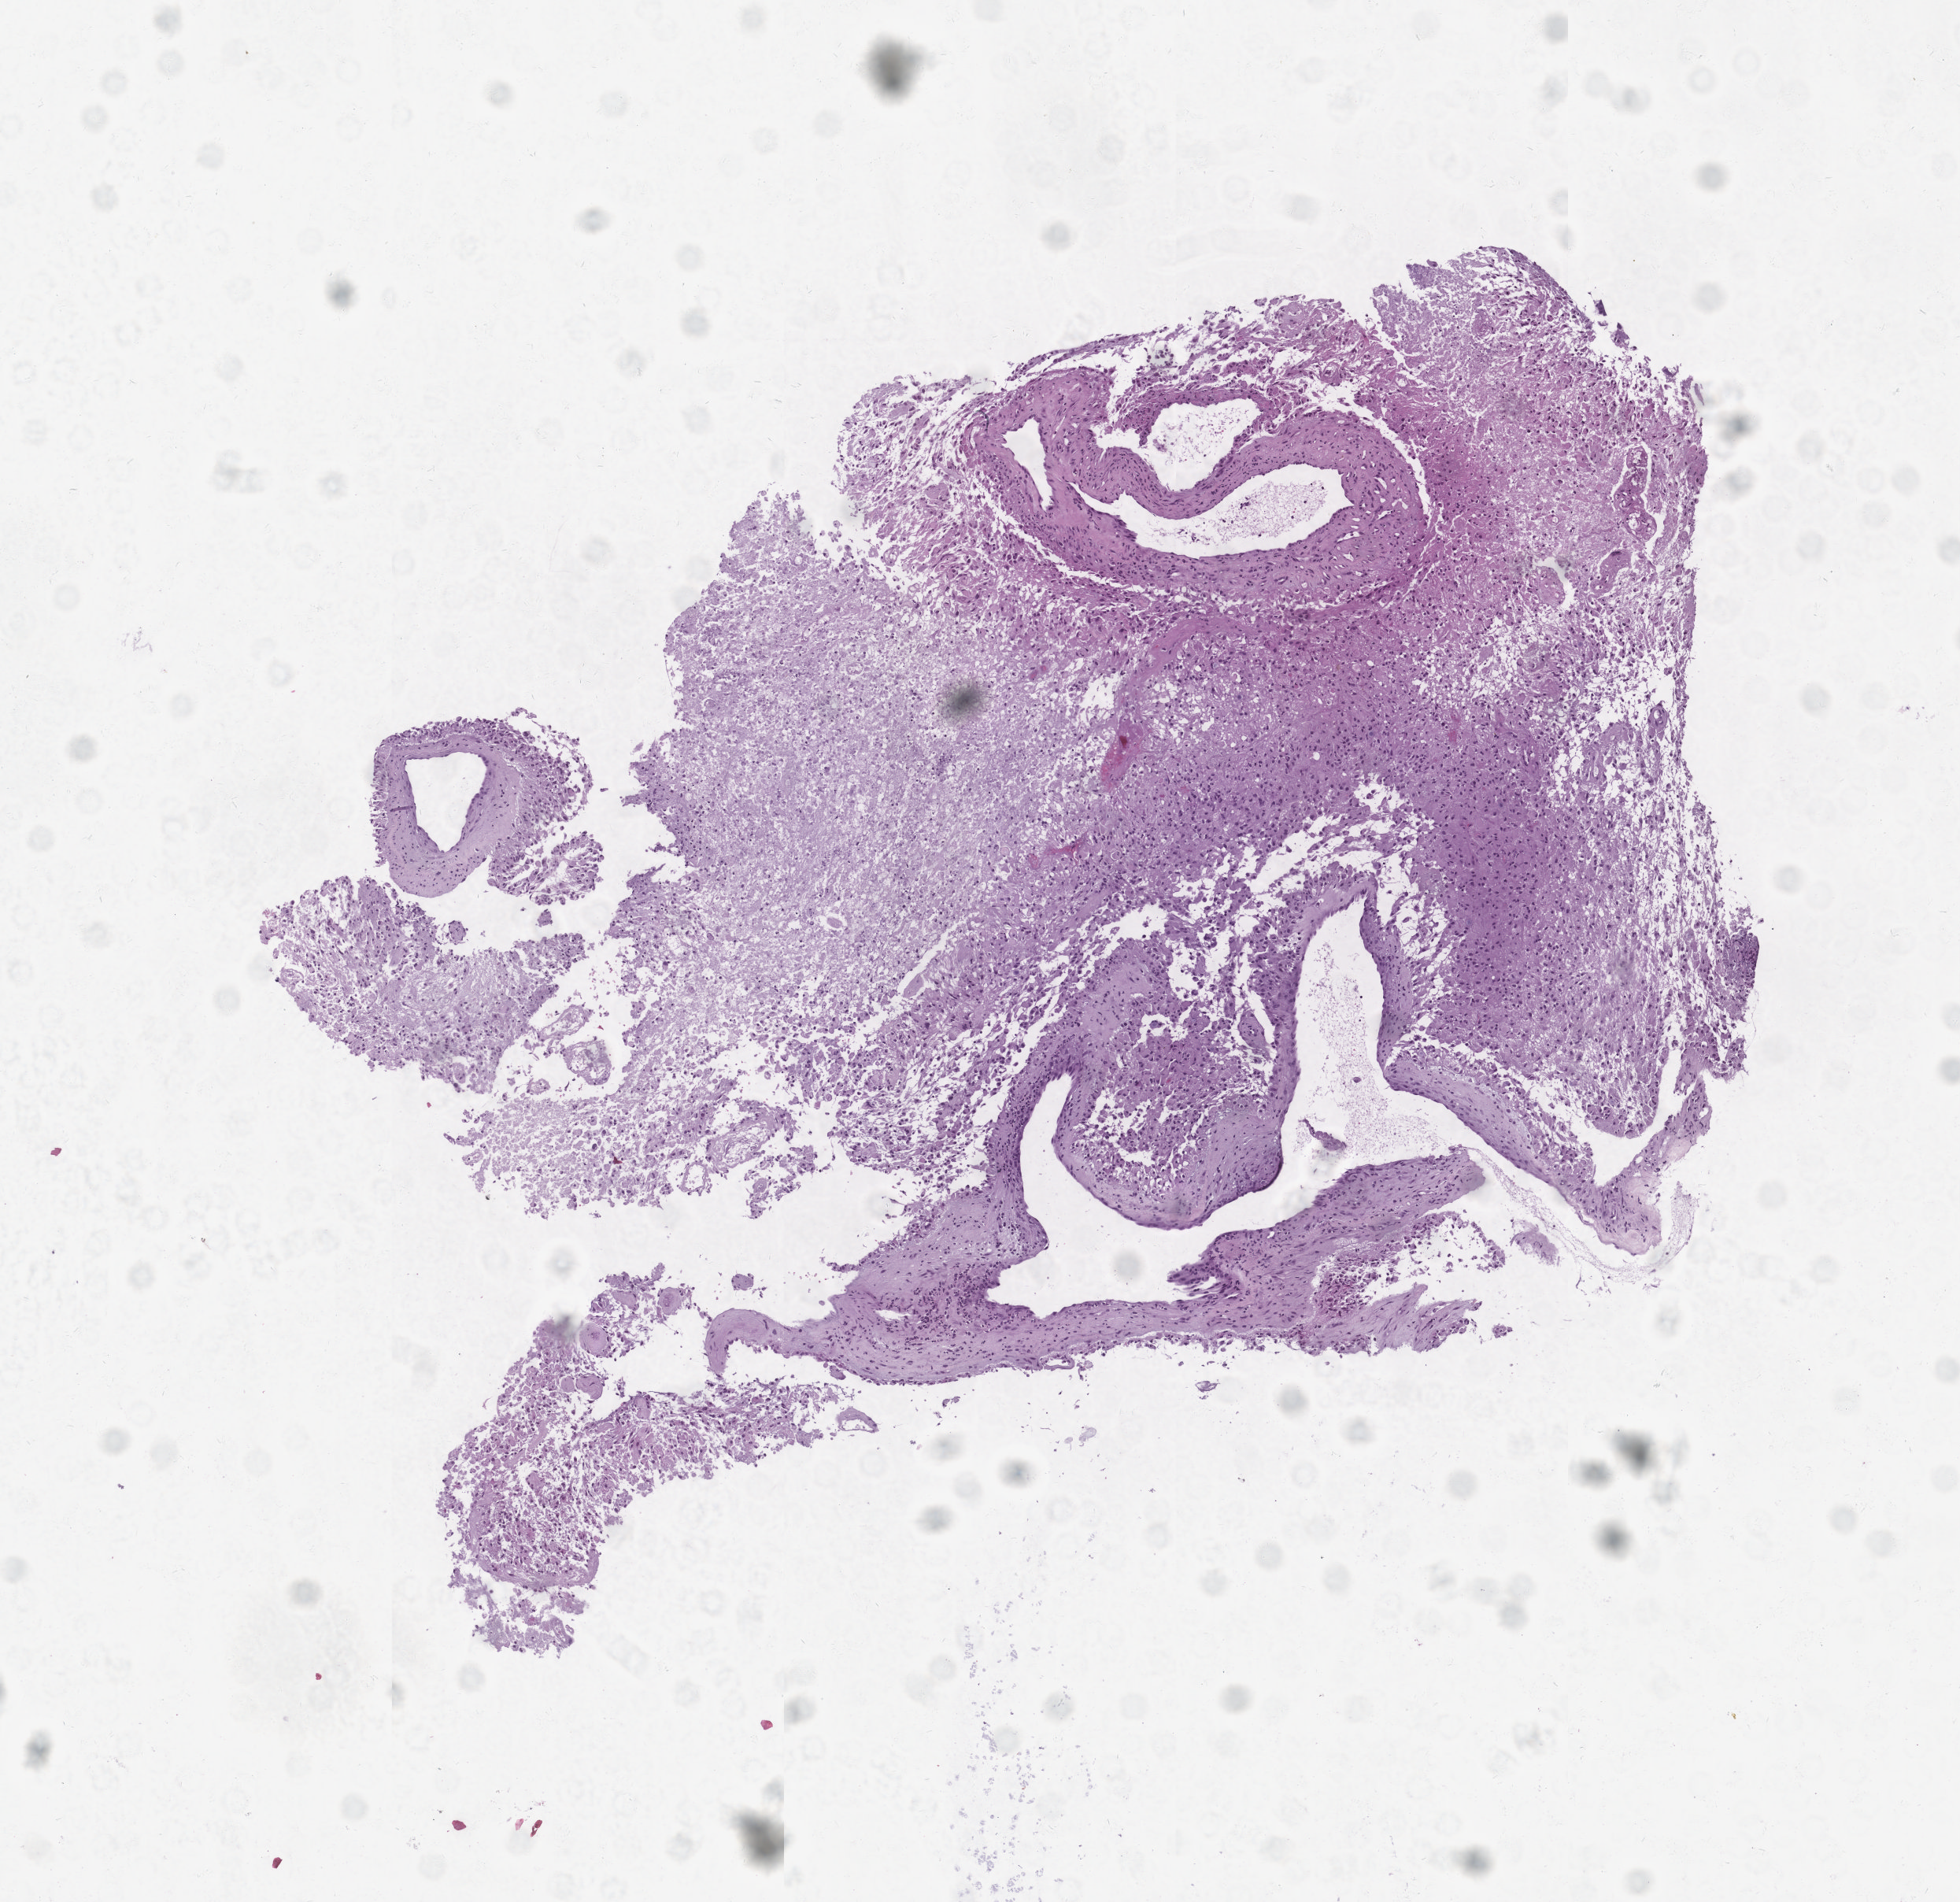
Whole-slide histology image, Hematoxylin and eosin (H&E) stained, a low-resolution overview of the entire scanned area, about 5.0 x 4.9 mm. Brain, tumour tissue. 78-year-old male patient.
Histologic diagnosis: Glioblastoma.